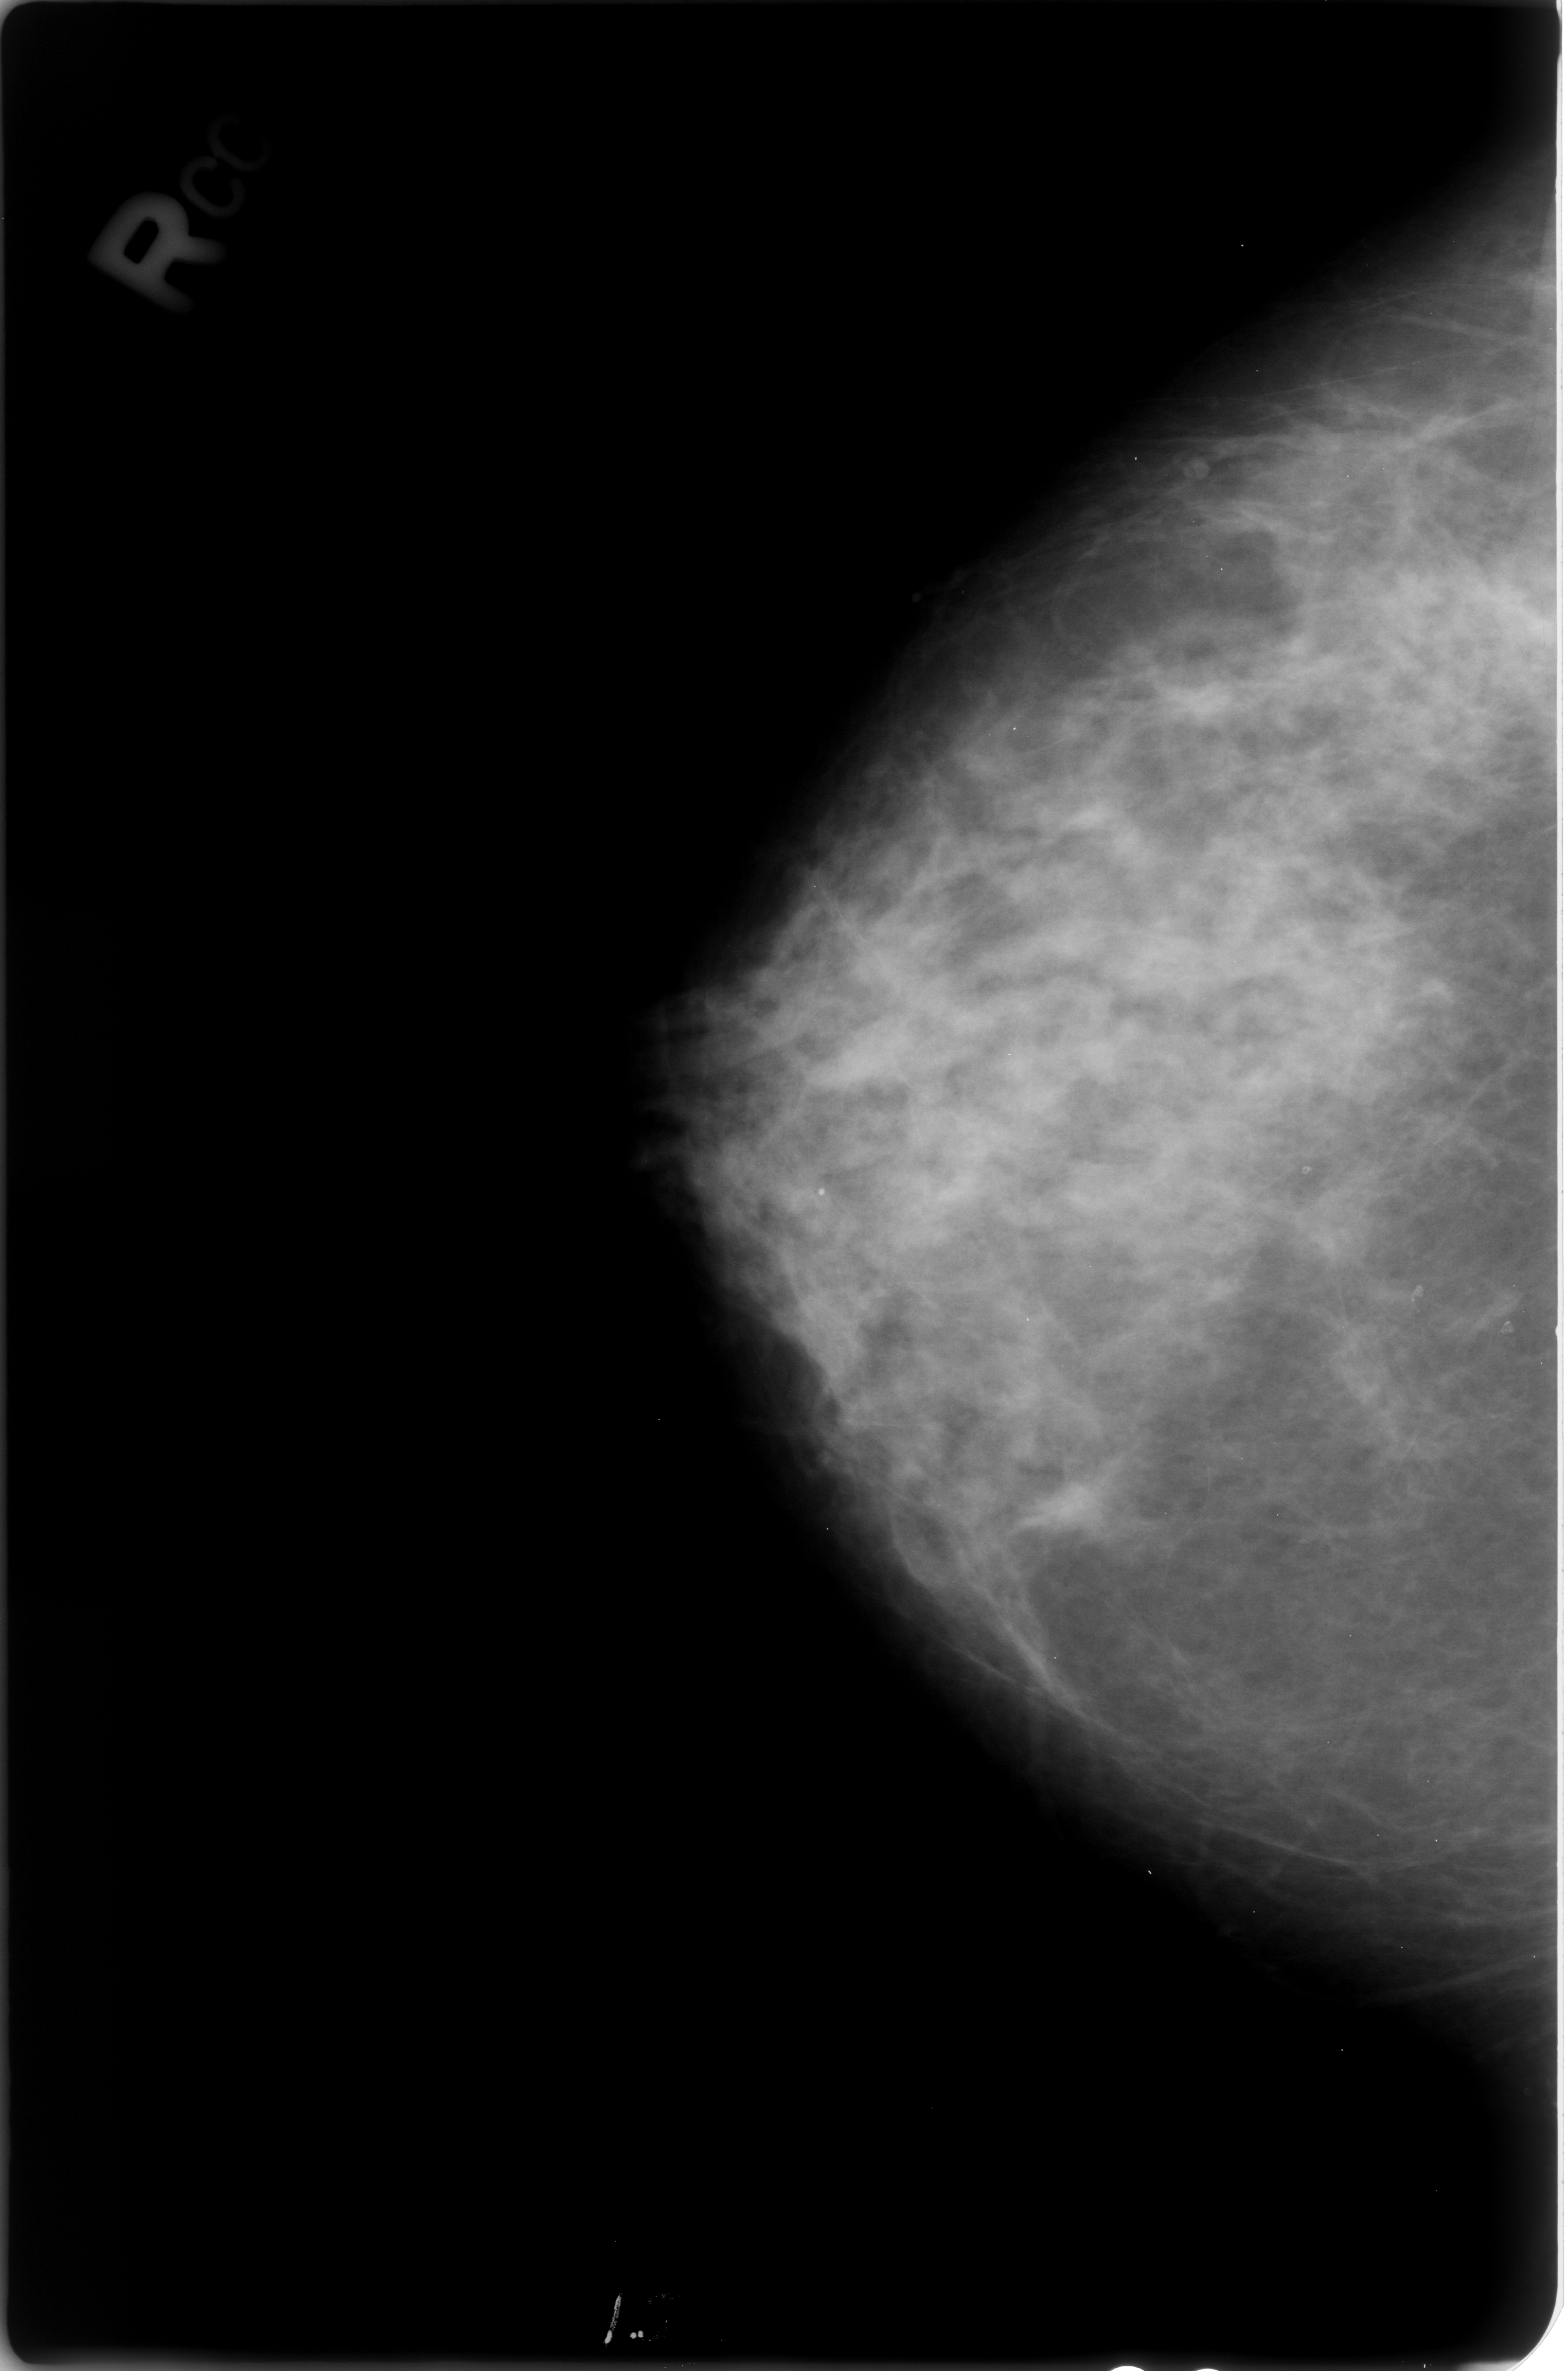
Digitized screen-film mammogram. Right breast. CC view. Breast composition: heterogeneously dense (BI-RADS density category 3 of 4). 1568 × 2371 image matrix.
Expert-marked regions of interest on this image (one box per marked abnormality):
- Finding 1 of 2: calcifications, morphology round and regular / lucent center; BI-RADS assessment category 2; benign; no additional work-up was recommended (outcome (as recorded, no biopsy): benign without callback): bounding box [x1, y1, x2, y2] px = [802, 1177, 836, 1211]
- Finding 2 of 2: calcifications, morphology round and regular / lucent center; BI-RADS assessment category 2; subtlety rating 3 on a 1 (subtle) to 5 (obvious) scale; benign; no additional work-up was recommended (outcome (as recorded, no biopsy): benign without callback): [1292, 1156, 1322, 1182]